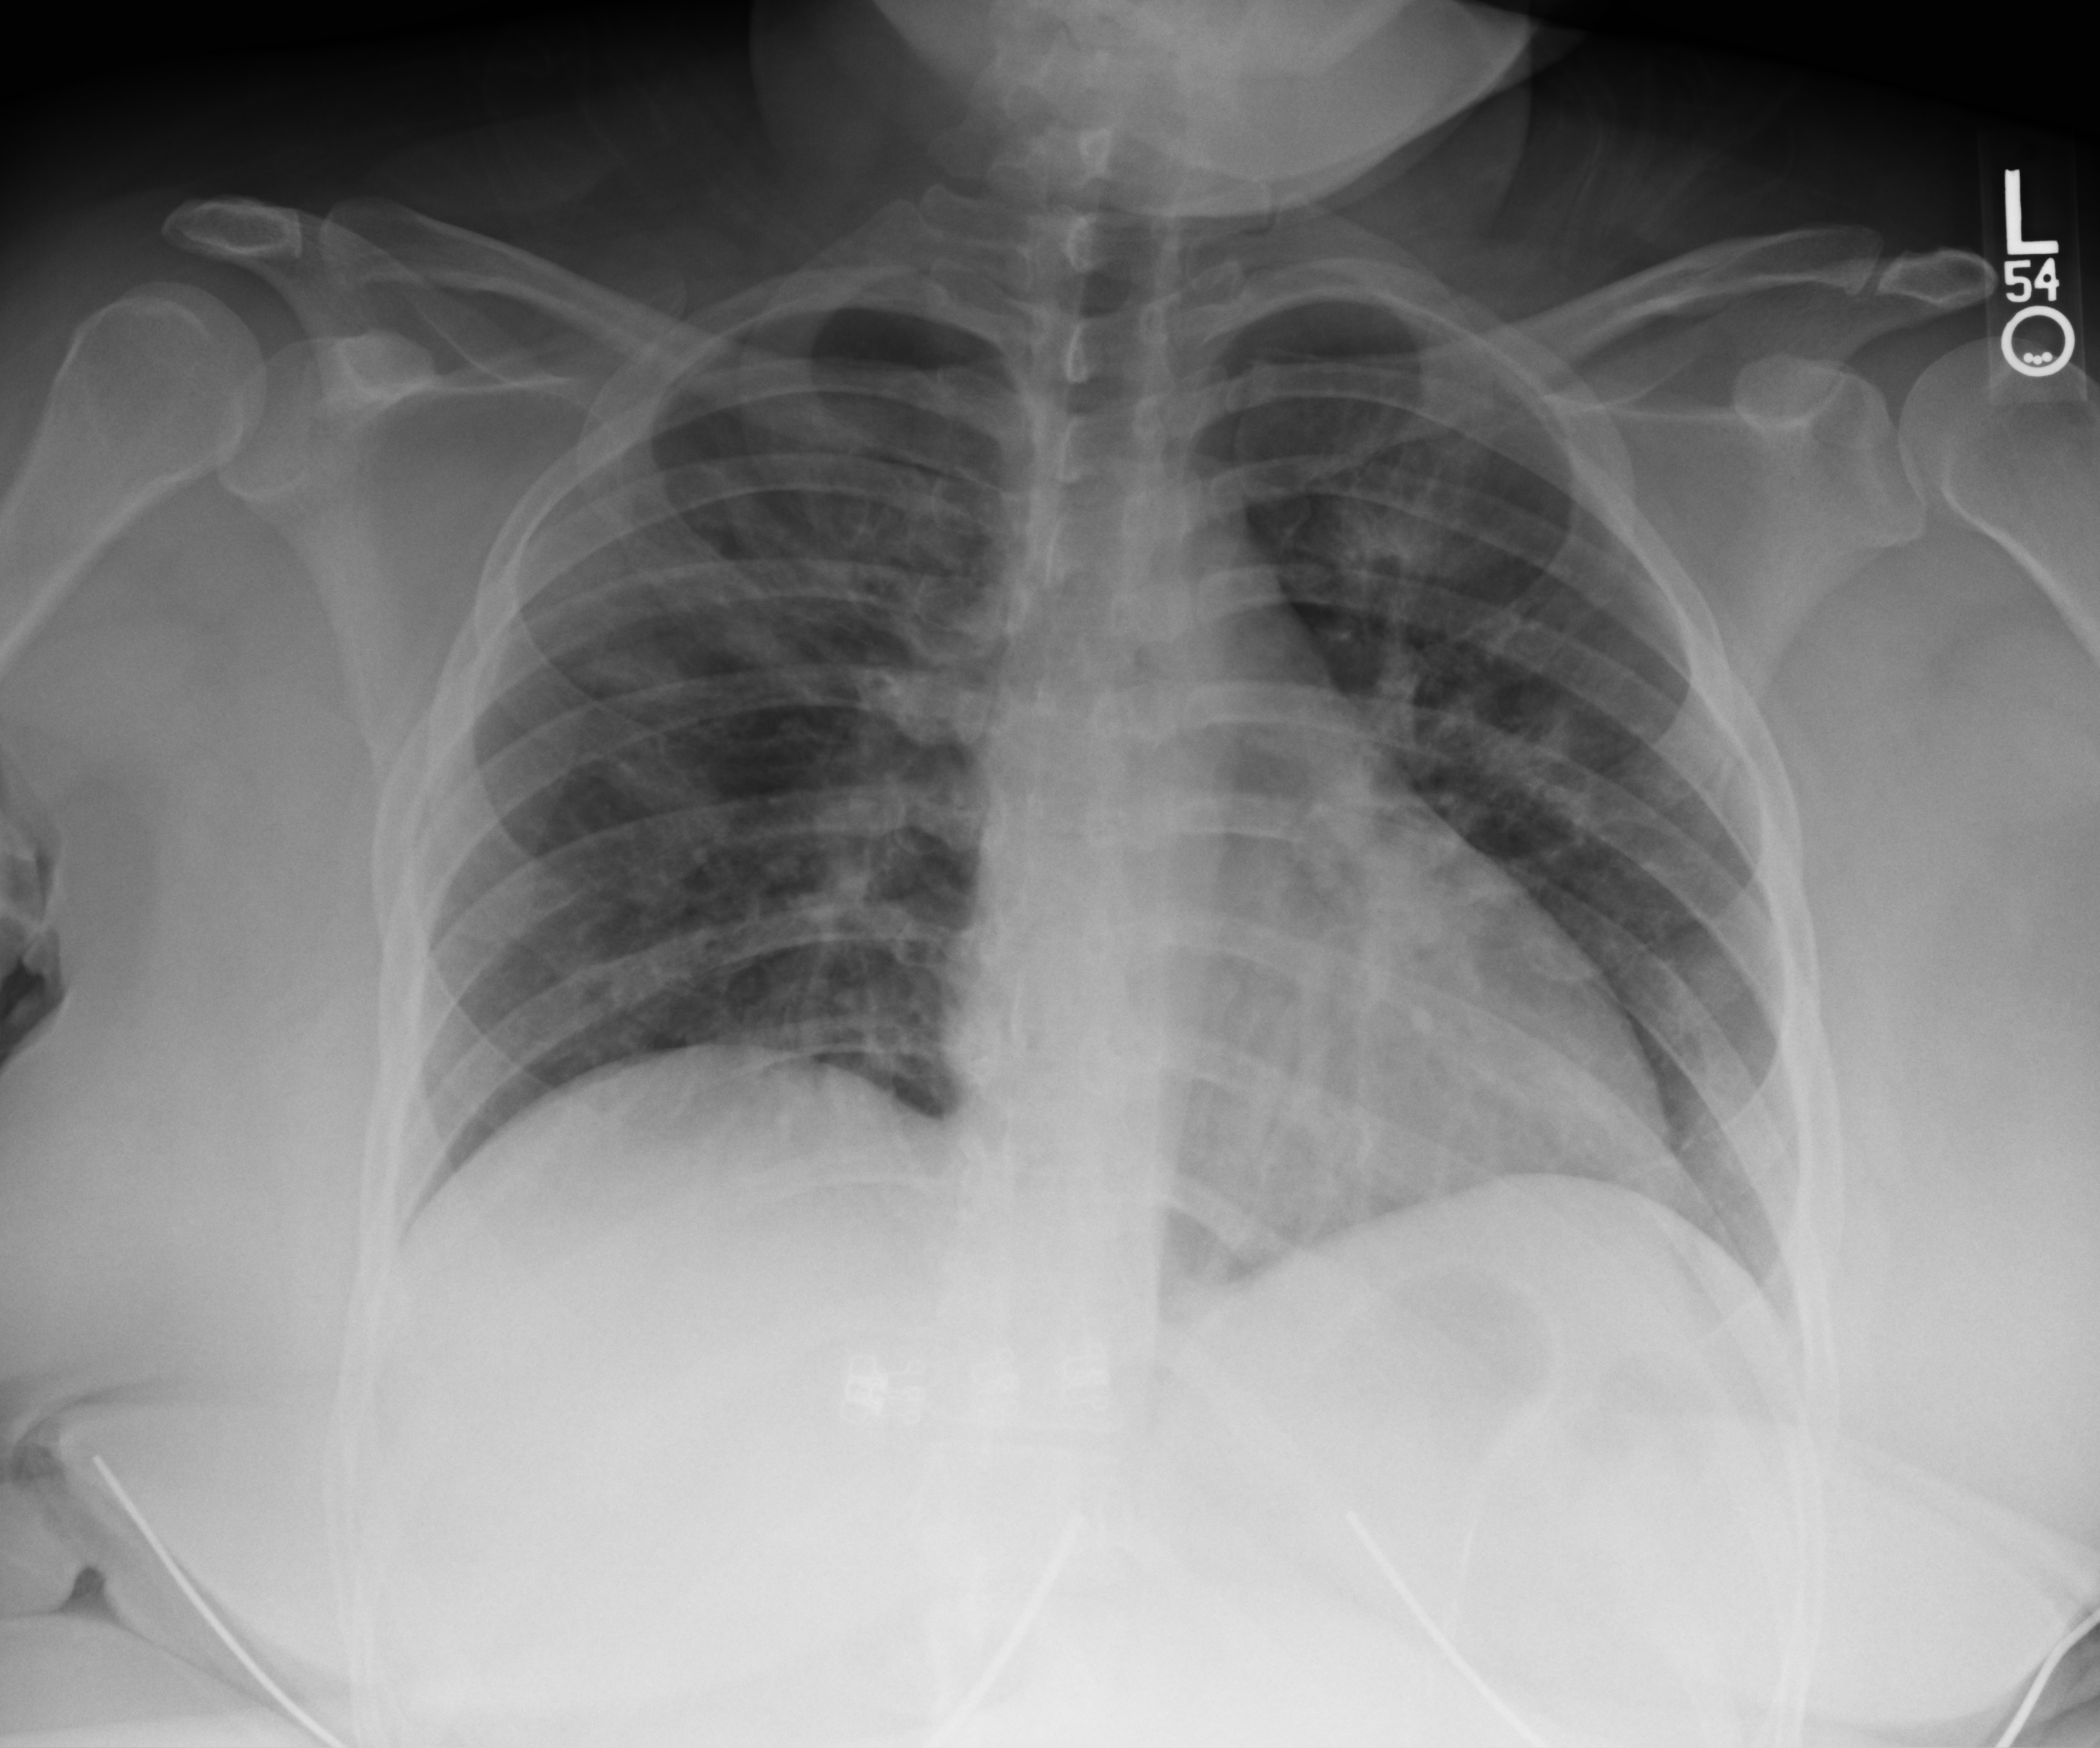
Chest X-ray (portable), anteroposterior (AP) projection. Patient hospitalised with COVID-19; female, aged 18–59 years.
Admission-level facts for this patient (not findings on this image; timing relative to this image not recorded): other chronic lung disease (admission record): no; hypertension (admission record): no.